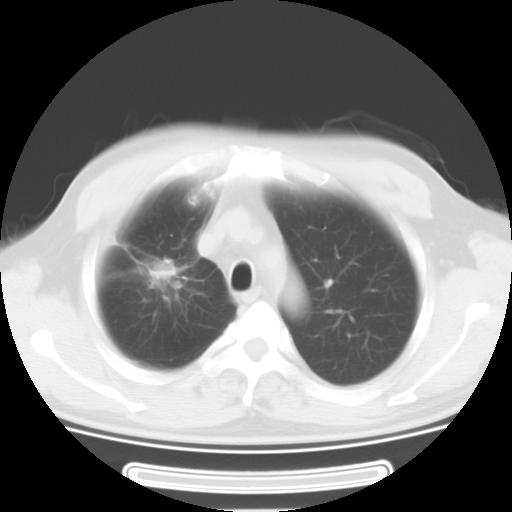
Chest CT, one axial slice. Slice 23 of 29 in the series (ordered by position). 120 kVp. Lung window (W 1500 / L -600 HU). 512 × 512 image matrix. Male patient, age 46 years. From the clinical record (not read from this slice): clinical TNM (as recorded): T3 N0 M1b.
Outlined on this slice (bounding box drawn by a radiologist):
- lung tumour (recorded histology: adenocarcinoma): bounding box <130,246,180,299> (left, top, right, bottom; pixels)